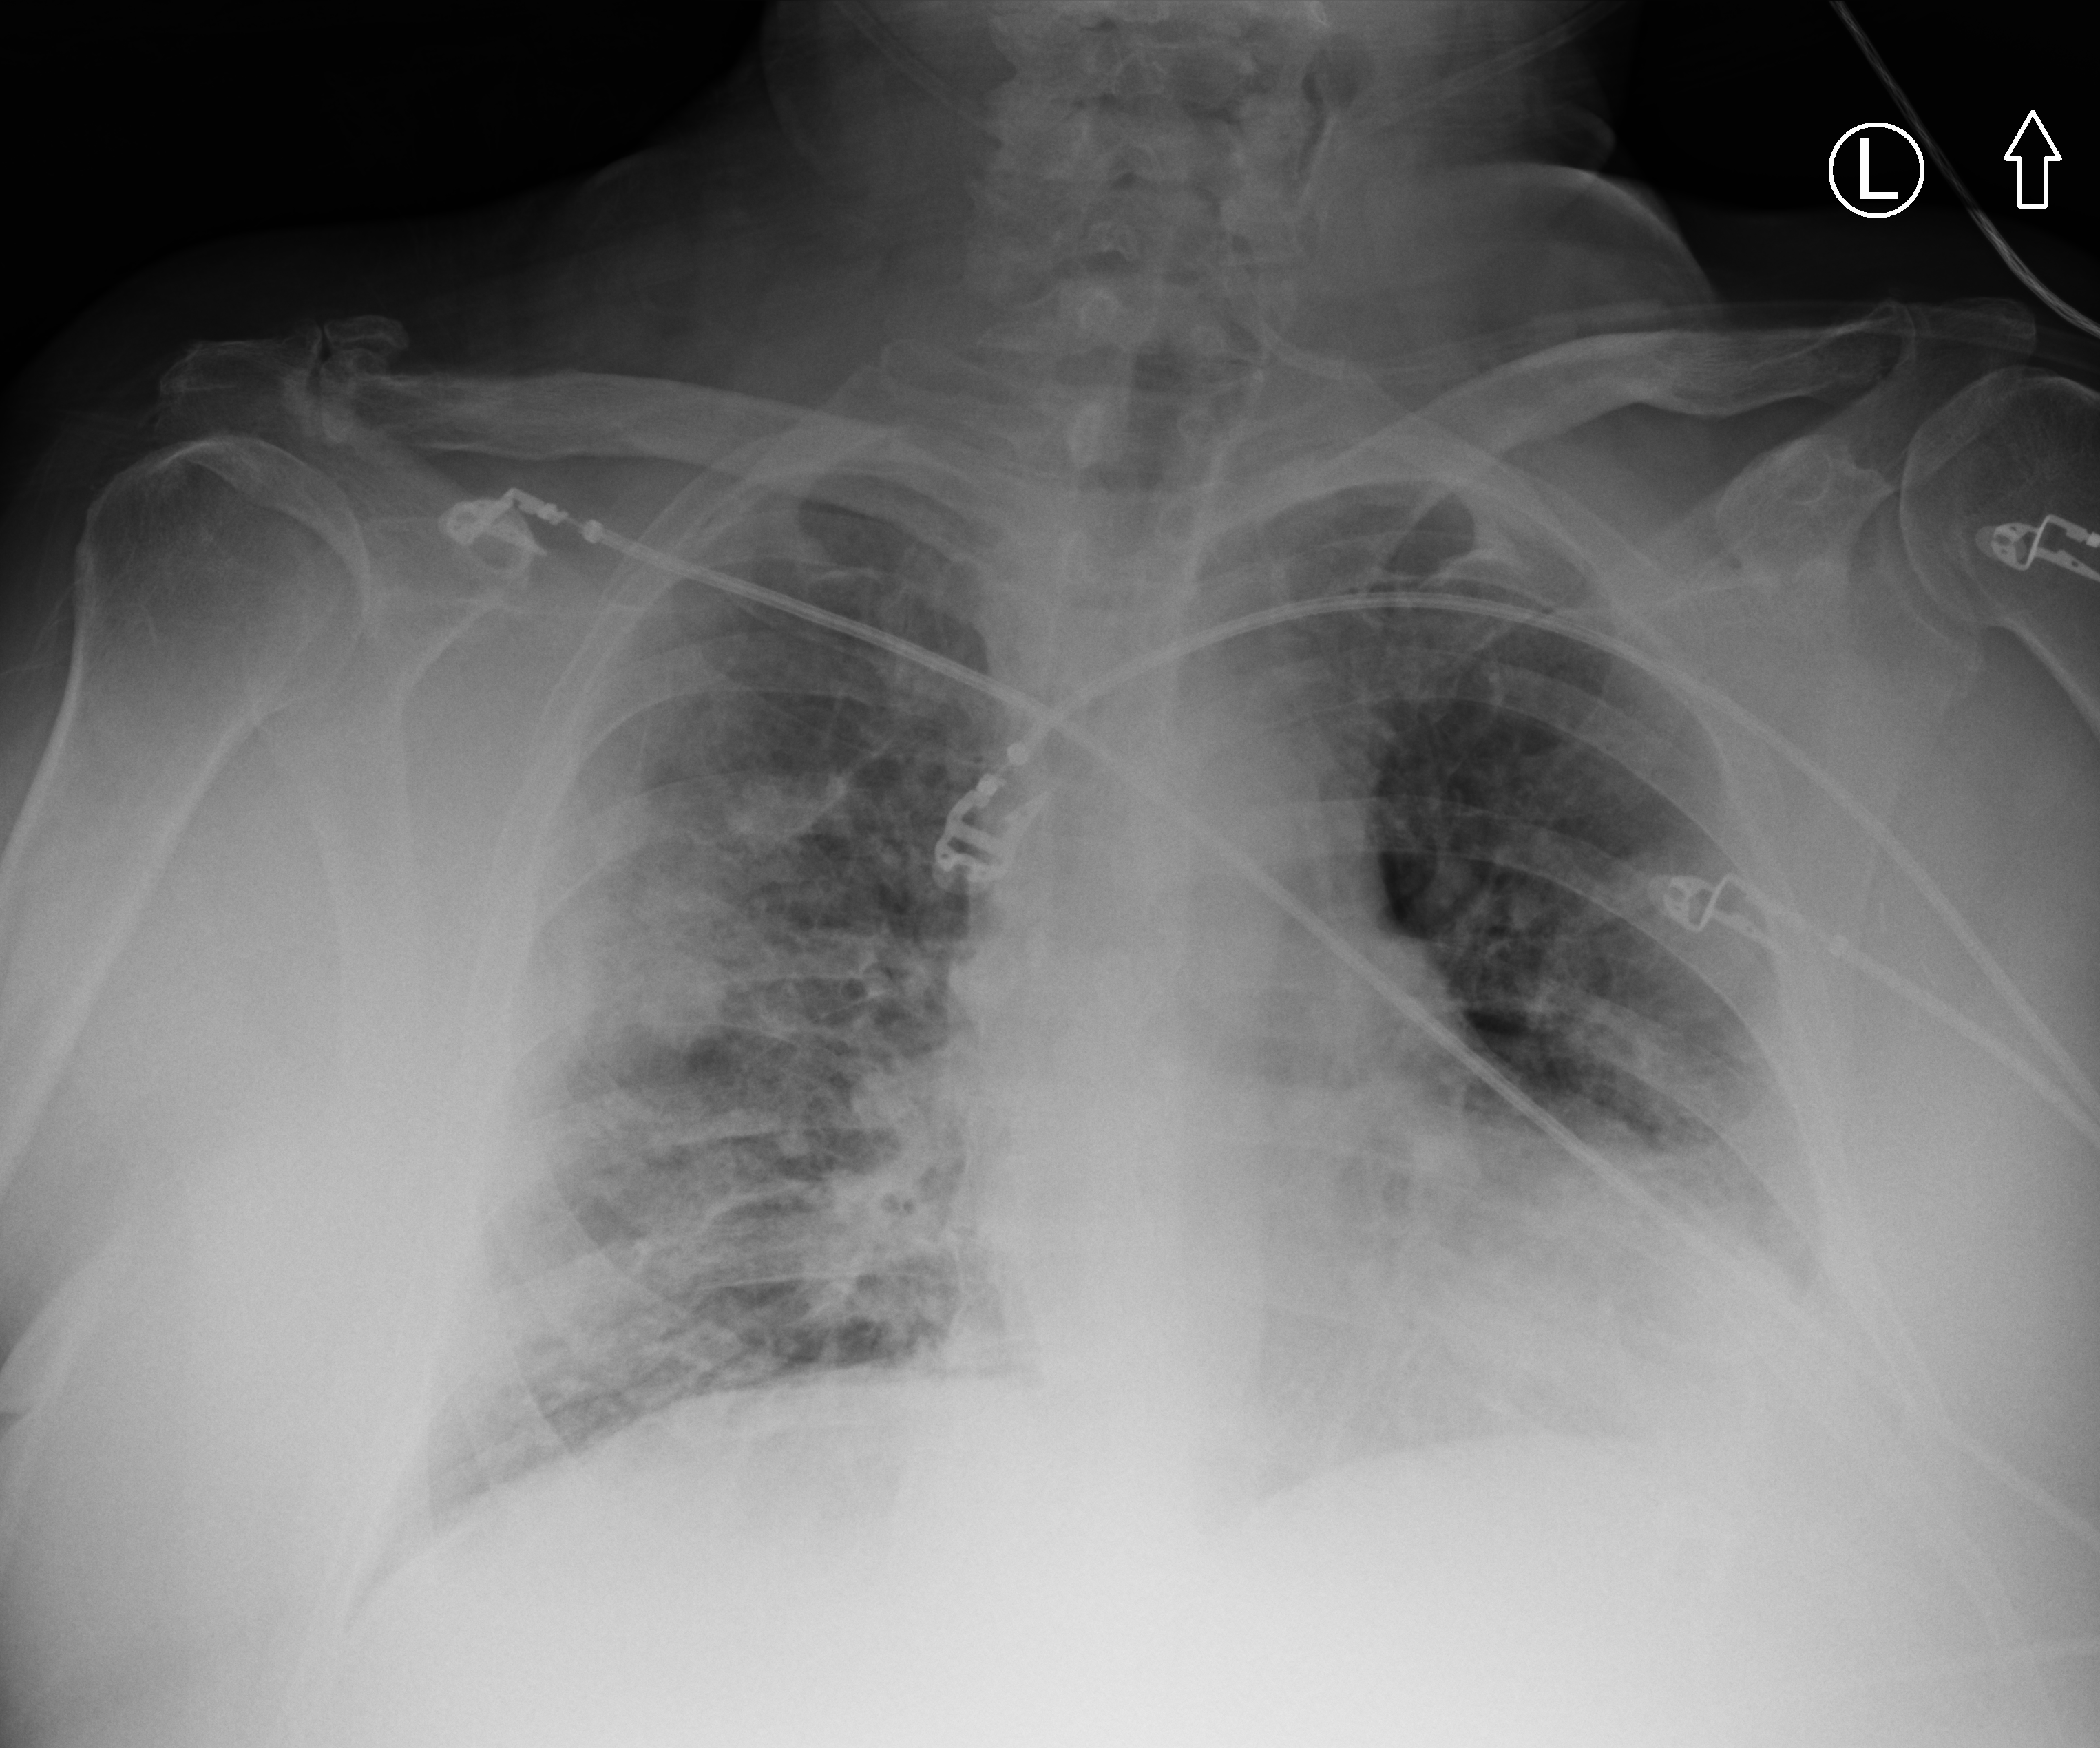
Portable chest radiograph, anteroposterior (AP) projection. Male patient hospitalised with COVID-19, age 60–74 years.
Hospital-stay facts (about this admission, not read from this image; timing relative to this image not recorded): mechanically ventilated during this hospital stay: yes; hypertension (admission record): yes; other chronic lung disease (admission record): no.